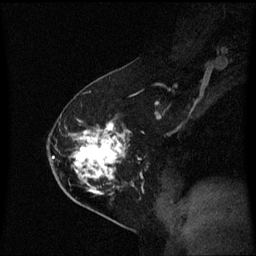
Breast MRI (dynamic contrast-enhanced), one sagittal slice. Slice 37 of 60 in the series (ordered by position). Dynamic contrast-enhanced series, image 2 of 3 at this slice position (ordered by acquisition). 1.5 T. TE 4.2 ms, TR 8.4 ms. 2 mm slice thickness. 256 × 256 image matrix. Patient: female, 54 years. Case-level facts recorded for this patient, not image findings: setting: breast cancer imaged before/during neoadjuvant chemotherapy; receptor status: HER2-positive.
Structures marked on this image (semi-automatic segmentation, software-assisted and operator-edited):
- analysis volume of interest (the breast-tissue region the enhancement analysis was run in; not a lesion): bounding box <59,124,140,199> (left, top, right, bottom; pixels)
- tumour enhancement mask (voxels above the 70 % enhancement threshold inside the analysis volume of interest): <74,124,126,195>